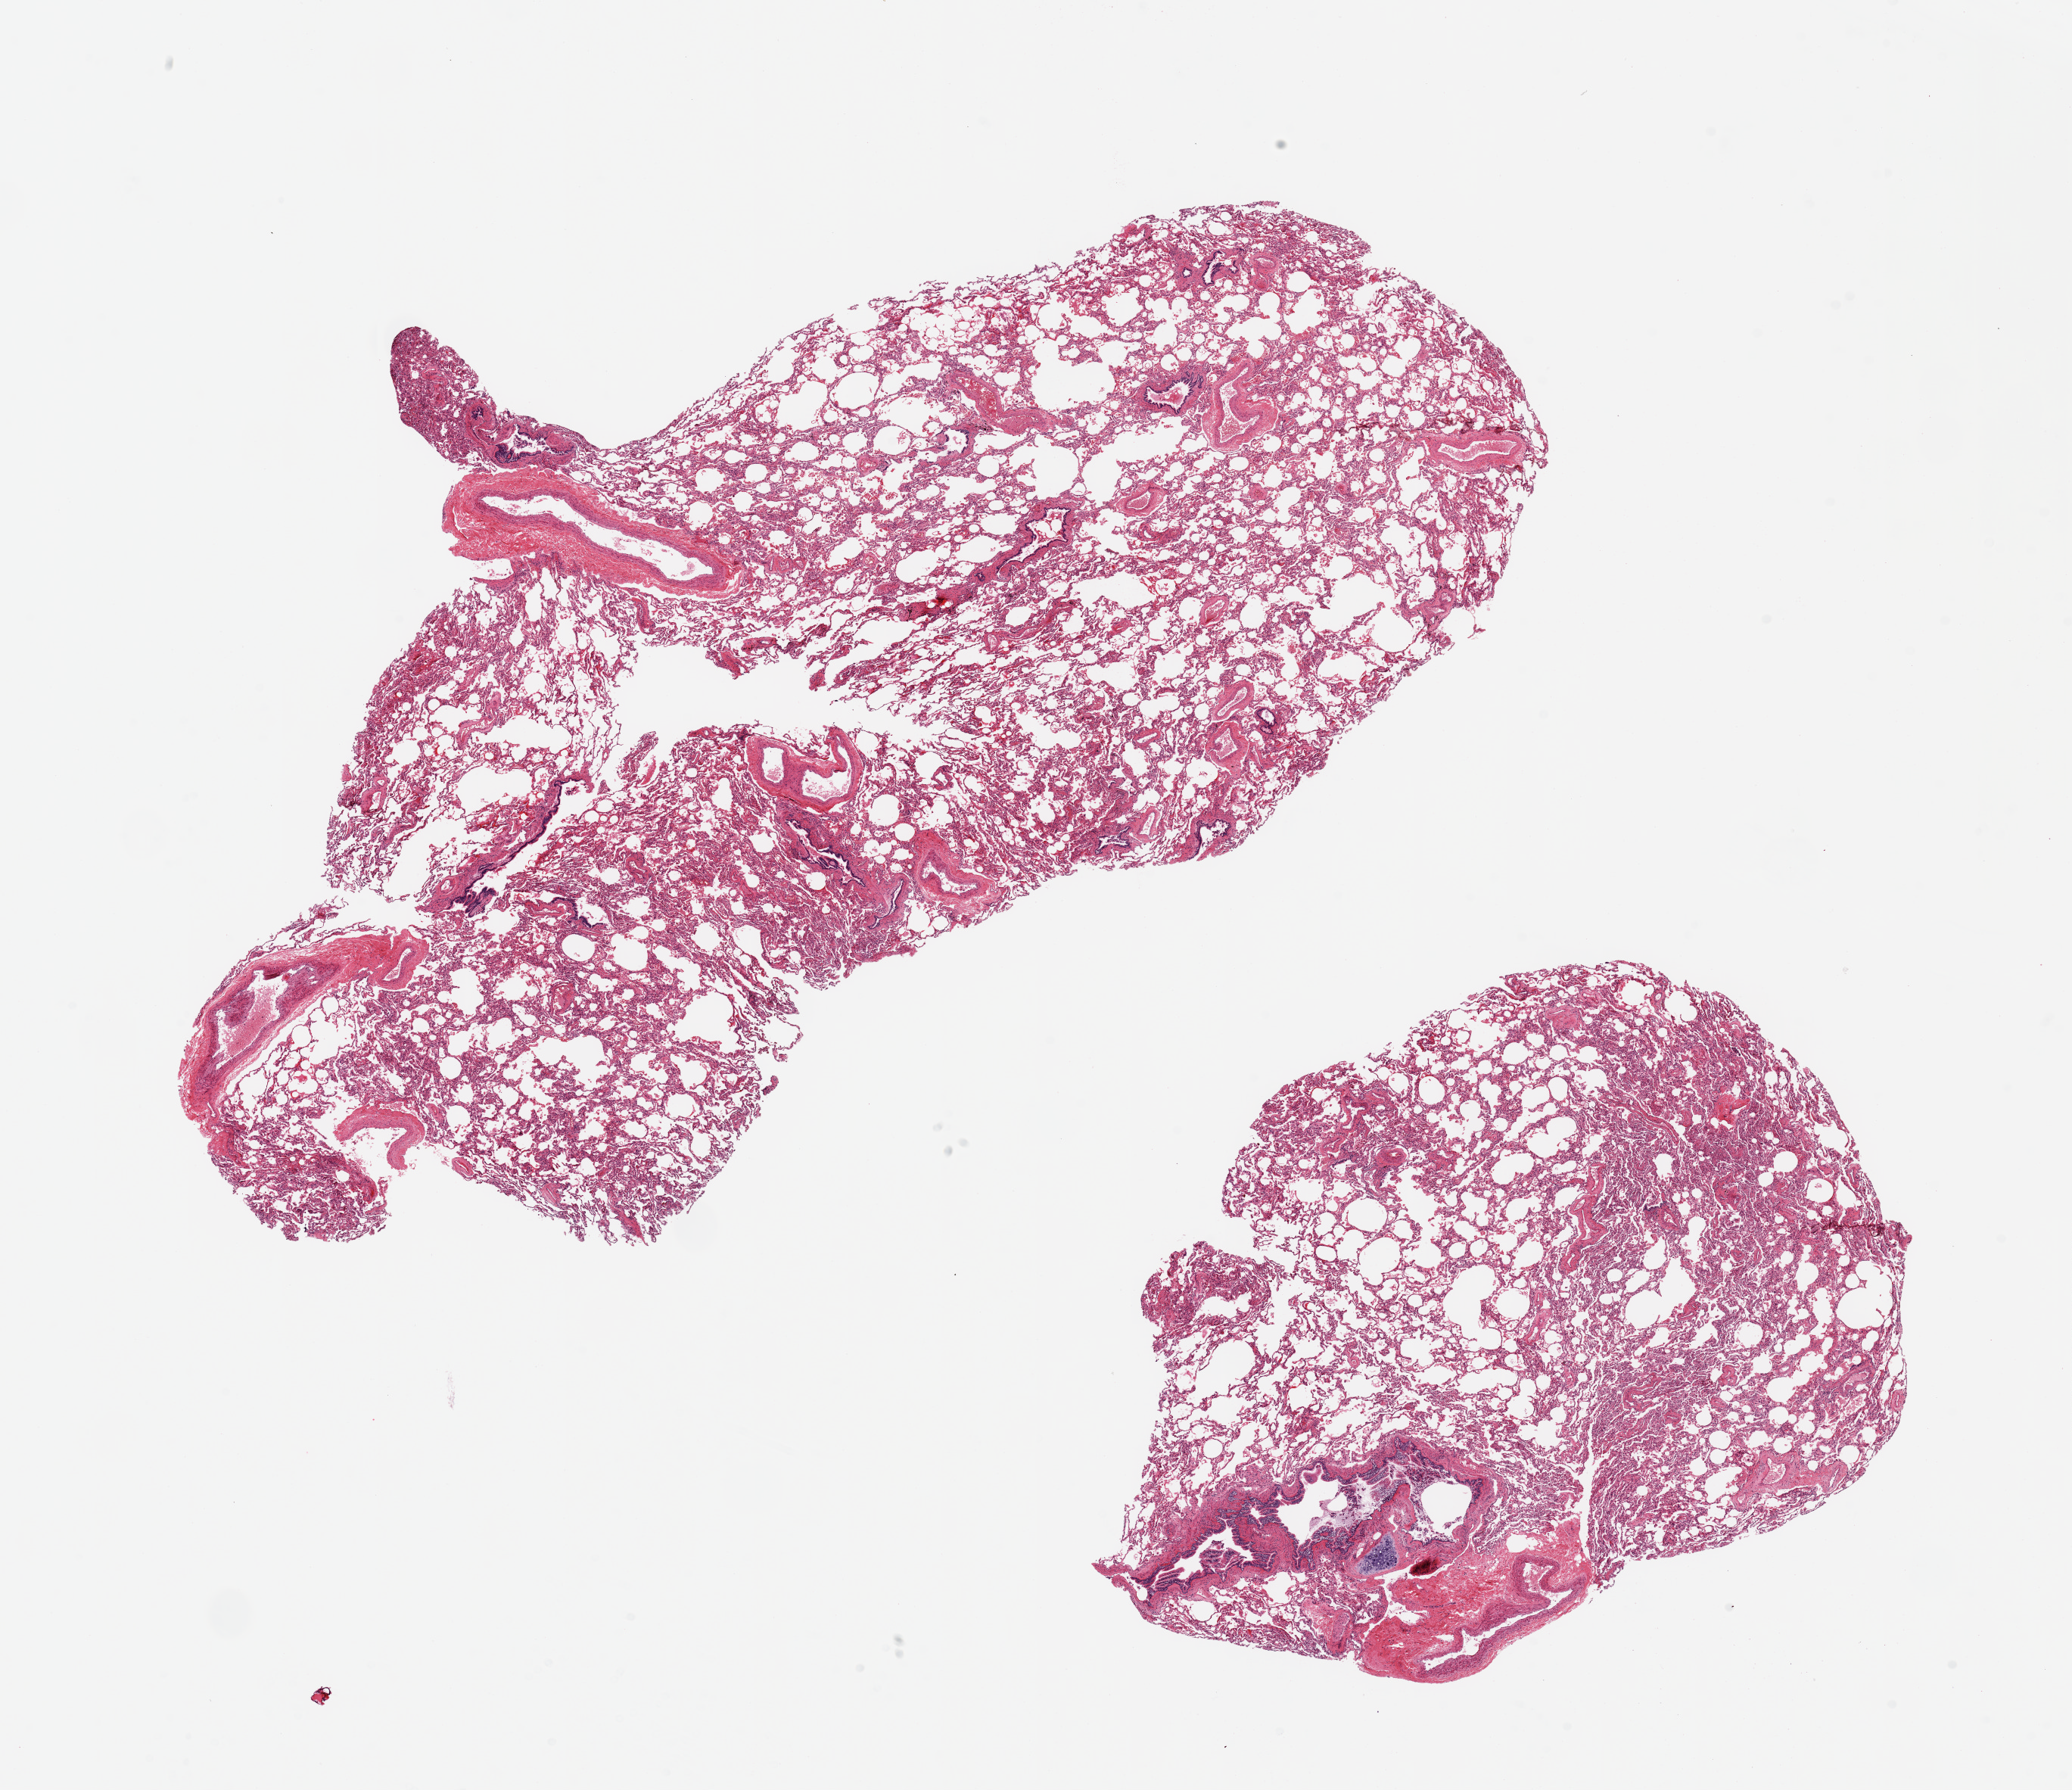
Hematoxylin and eosin (H&E) whole-slide image, whole scanned area (about 21.7 x 18.7 mm) shown as a low-resolution overview; PAXgene-fixed paraffin-embedded (PFPE) section; target tissue: lung; donor tissue sample. Donor: male.
Pathologist's review note for this sample: 2 pieces, ~12x6mm bronchial mucosa seen; Minimal congestion, well preserved.